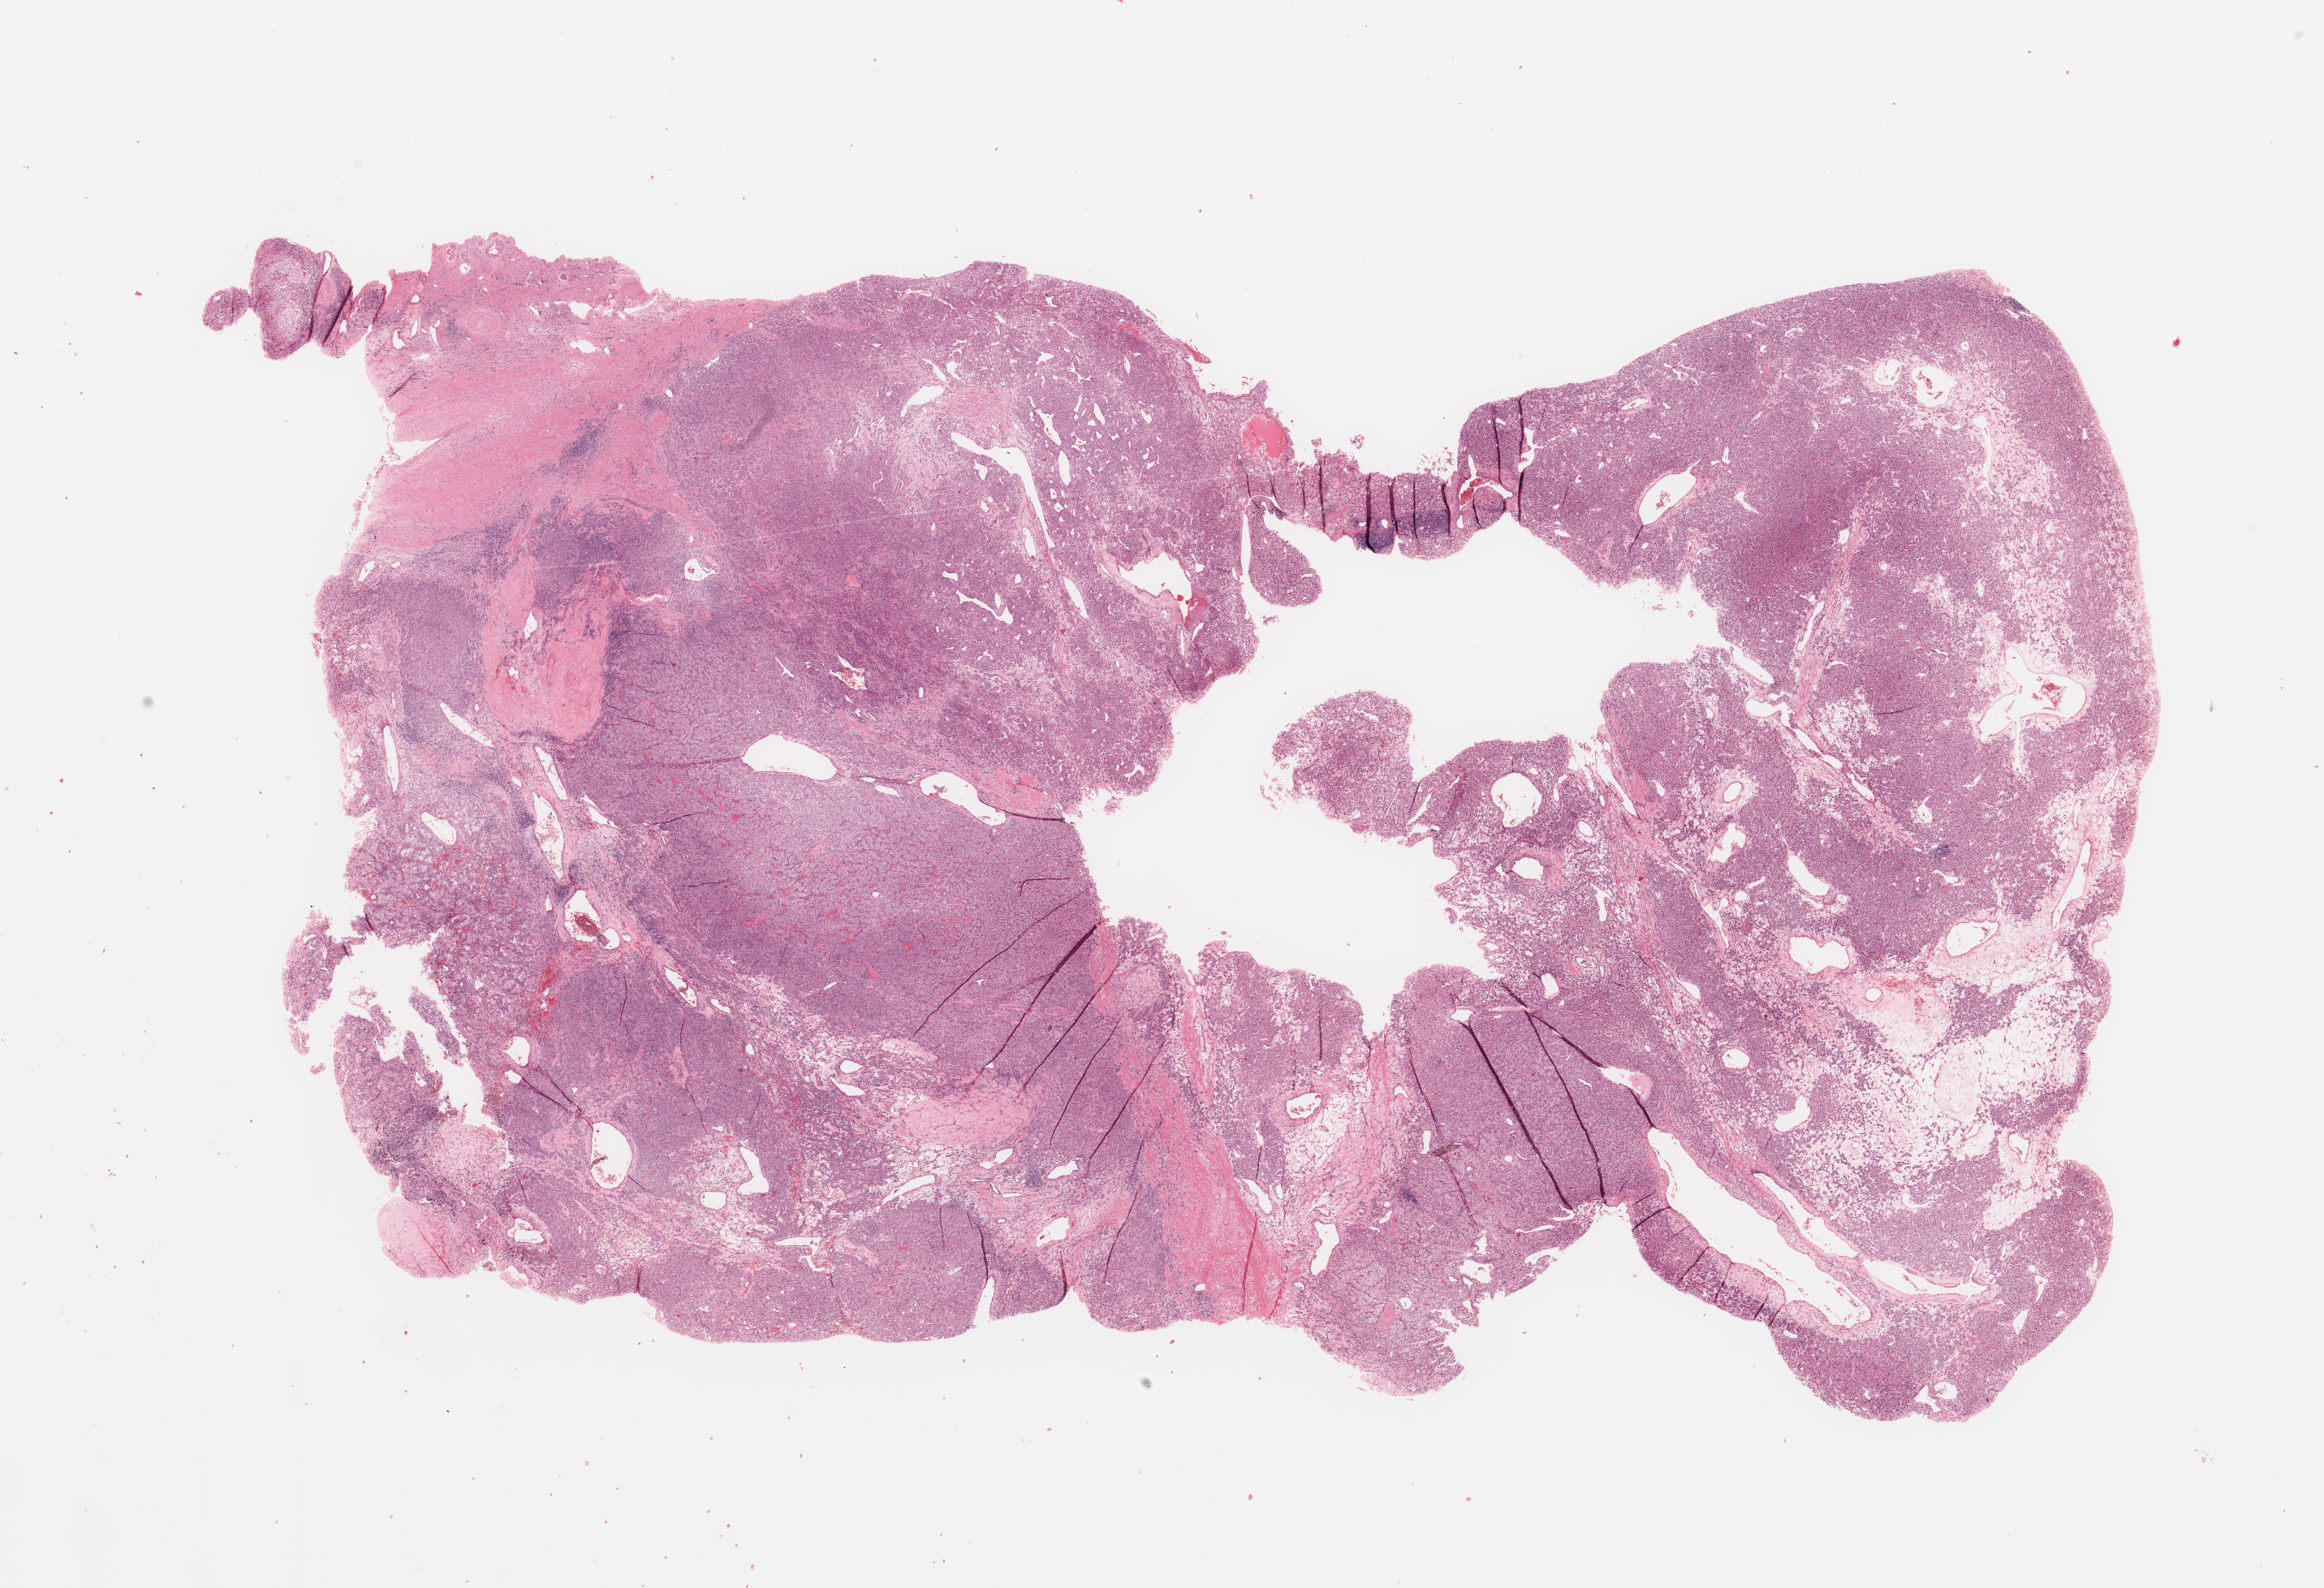
Digitized H&E-stained tissue section (whole slide) — low-resolution overview of the scanned area, about 22.6 x 15.5 mm (slide scanned at 20x), tumour tissue sample, sampled site: kidney. Patient: male, age 52 years. Histologic grade: G2 (moderately differentiated). Slide review estimates, as recorded: tumour nuclei 80%, necrosis 5%.
- diagnosis: Renal cell carcinoma, NOS
- AJCC pathologic stage: I
- primary tumour site (as recorded): upper pole